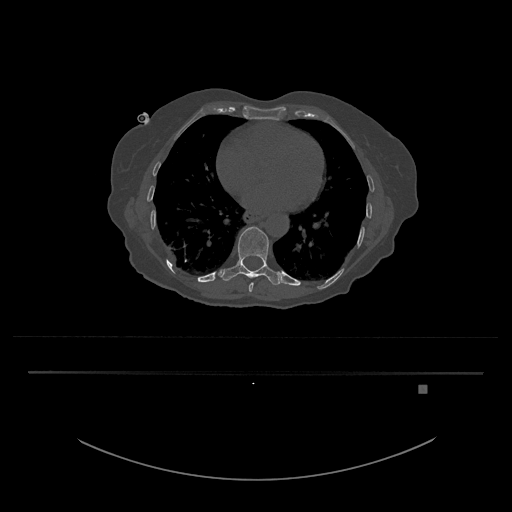
CT including the spine, one axial slice; position 722 of 797 along the scan axis; reconstruction kernel Br40s/3; bone window (W 1800 / L 400 HU); 0.5 mm slice thickness; 512 × 512 image matrix, field of view 500 × 500 mm. Patient: female, 57 years. From the clinical record (not read from this slice): primary cancer: cervical.
Annotated regions visible in this slice (semi-automatic segmentation, software-assisted and operator-edited):
- T10 vertebra: bounding box [x1, y1, x2, y2] px = [221, 226, 285, 285]
- T9 vertebra: [248, 282, 254, 292]